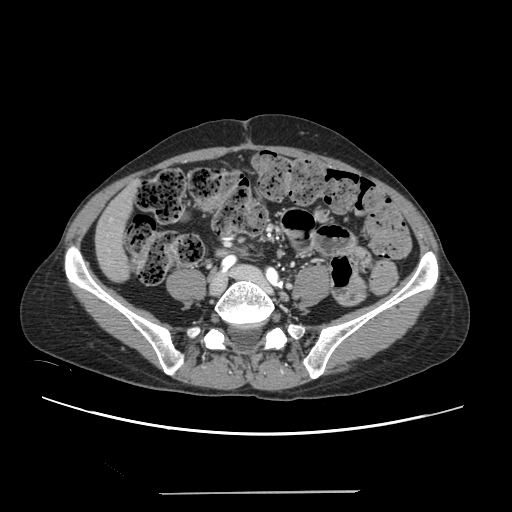
Contrast-enhanced abdominal CT, one axial slice. Slice 22 of 240 in the series (ordered by position). 120 kVp. Soft-tissue window (W 400 / L 40 HU). 1.25 mm slice thickness. 512 × 512 image matrix, field of view 371 × 371 mm. Female patient, age 60 years. Case-level facts recorded for this patient, not image findings: diagnosis: colorectal cancer liver metastases, imaged before liver resection; multiple liver metastases: no; largest metastasis: 1.5 cm; disease in both lobes: no.
Structures marked on this image (manually delineated by an expert):
- liver: box from (x=97, y=186) to (x=135, y=280) px
- planned liver remnant (the part of the liver to remain after resection): (x=97, y=186)–(x=135, y=280)
- portal vein (with intrahepatic branches): (x=110, y=218)–(x=112, y=220)